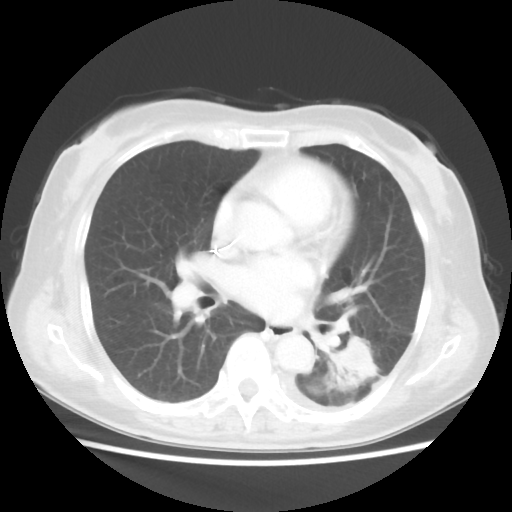
Chest CT, one axial slice; position 18 of 40 along the scan axis; reconstruction kernel STANDARD; 100 kVp; lung window (W 1500 / L -600 HU); 512 × 512 image matrix, field of view 341 × 341 mm. Patient: female, 69 years. Case-level facts recorded for this patient, not image findings: clinical TNM (as recorded): T1c N0 M0.
Outlined on this slice (bounding box drawn by a radiologist):
- lung tumour (recorded histology: adenocarcinoma): bounding box <331,330,375,386> (left, top, right, bottom; pixels)